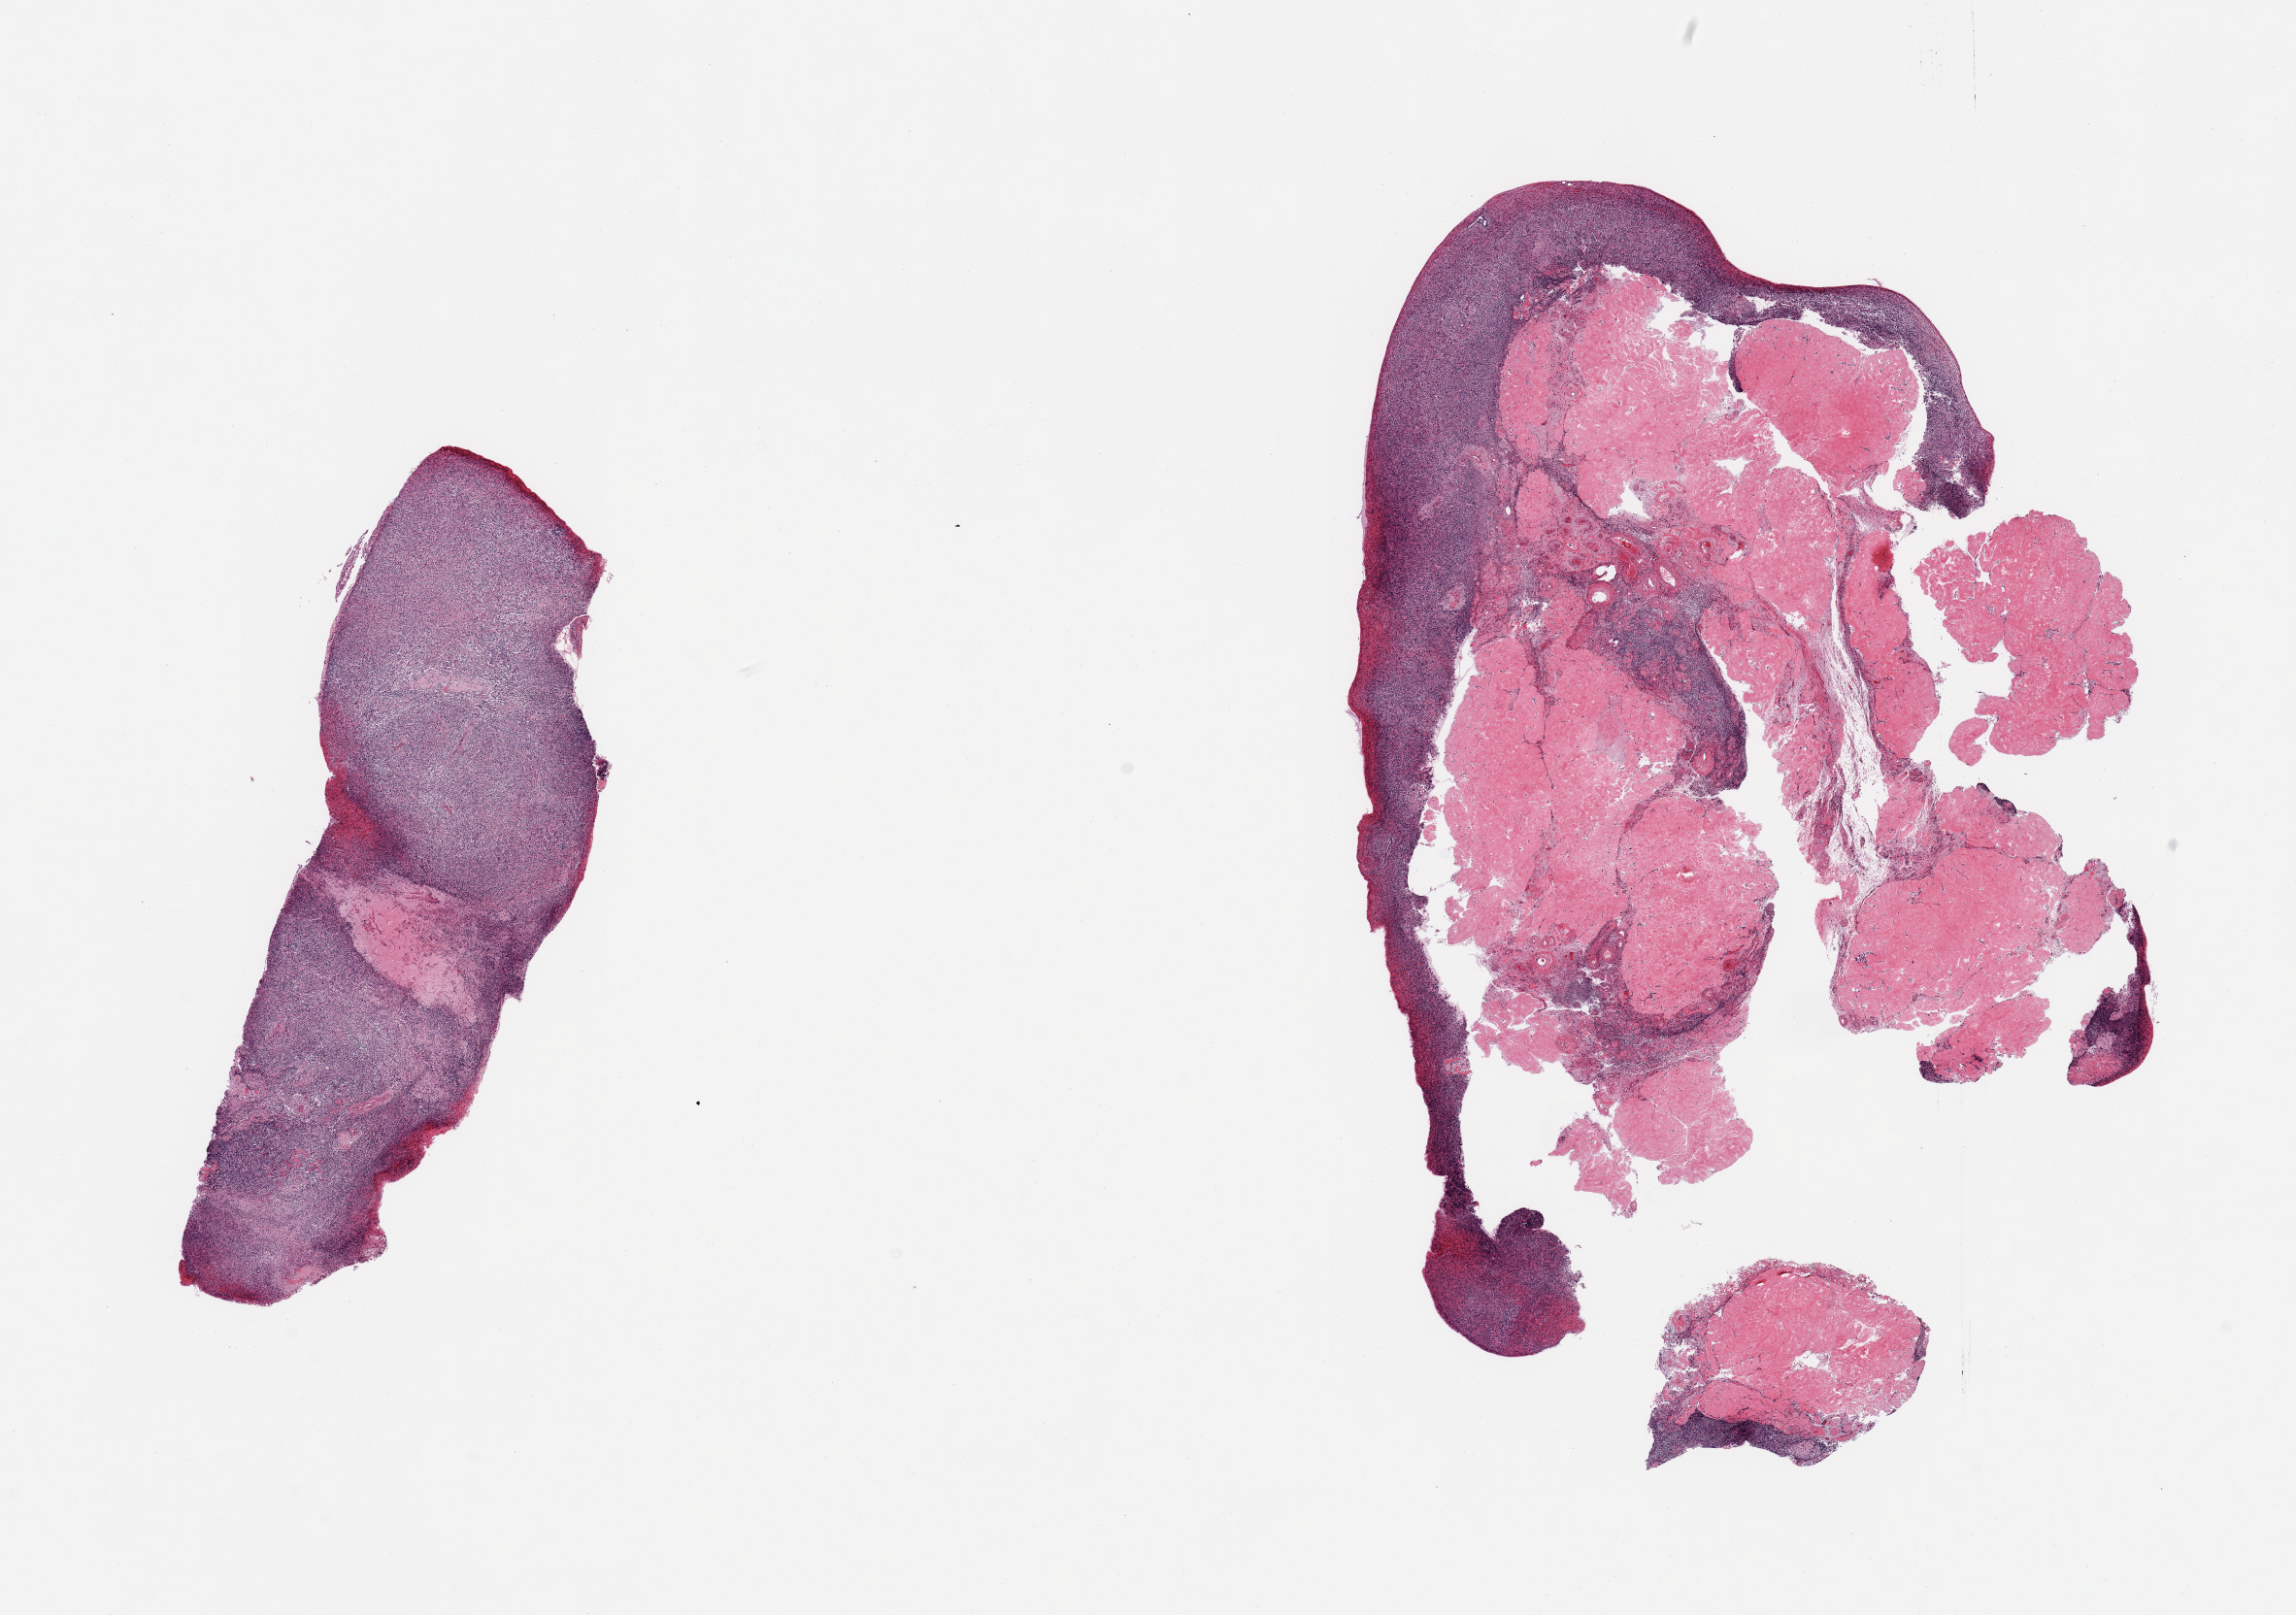
Hematoxylin and eosin (H&E) whole-slide image — whole scanned area (about 18.7 x 13.2 mm) shown as a low-resolution overview, PAXgene-fixed paraffin-embedded (PFPE) section, section of ovary (target tissue), tissue donor sample. Donor sex: female.
• pathologist's review note for this sample: 2 pieces, 1 with 80% corpora albicans, other [smaller] with 10%